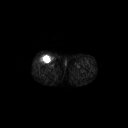
FDG PET of an extremity soft-tissue mass (from a PET/CT study), one axial slice. Position 269 of 311 along the scan axis. 3.27 mm slice thickness. 128 × 128 image matrix. Male patient, age 56 years. From the clinical record (not read from this slice): histological type: pleiomorphic leiomyosarcoma; grade: intermediate; site of the primary tumour: right thigh.
Annotated regions visible in this slice (expert contour drawn on MRI and transferred to this co-registered scan by the dataset authors):
- gross tumour volume including surrounding oedema: box from (x=40, y=54) to (x=51, y=63) px
- gross tumour volume (mass): (x=40, y=55)–(x=51, y=63)